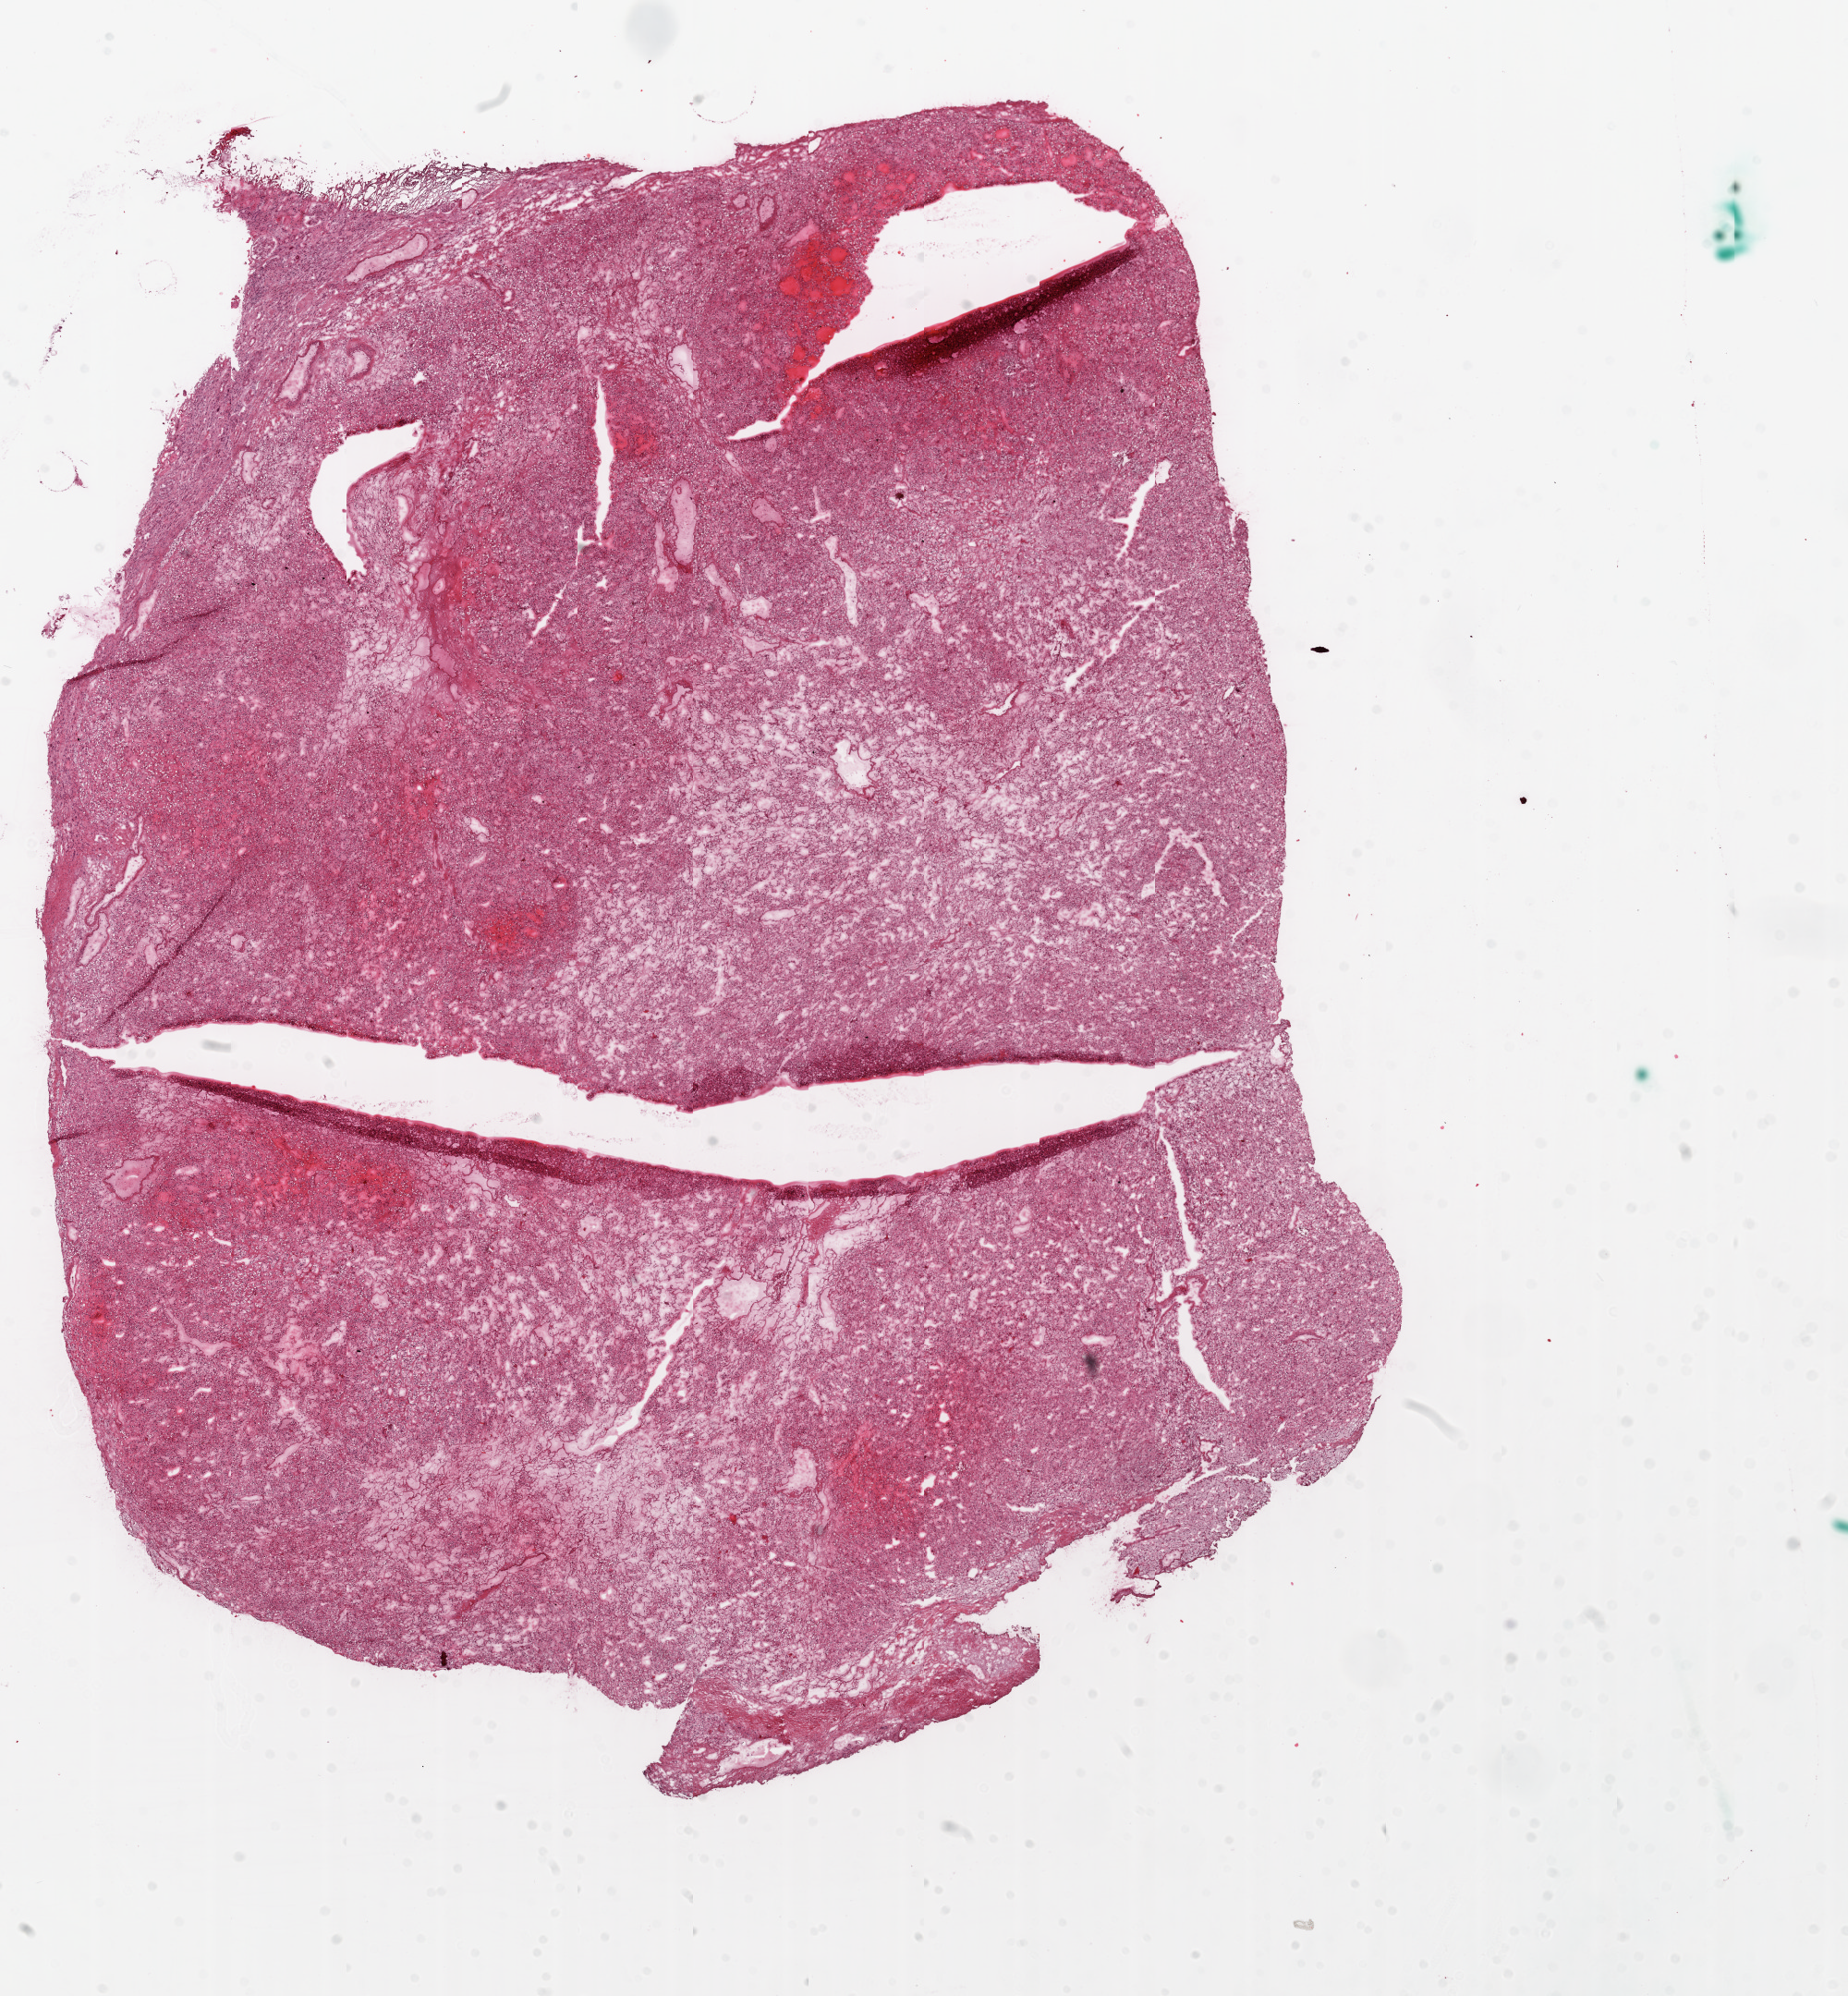
Hematoxylin and eosin (H&E) stained whole-slide image, shown as a low-resolution overview of the whole scanned area (about 16.0 x 17.3 mm). Frozen section from the top of the tissue portion. Sample: primary tumour, kidney. Female patient; age at initial diagnosis 63 years. Histologic grade: G2 (moderately differentiated). Slide review estimates, as recorded: tumour cells 85%, tumour nuclei 80%, normal cells 5%, stromal cells 10%, necrosis 0%.
Histologic diagnosis: Clear cell adenocarcinoma, NOS. AJCC pathologic stage: I.